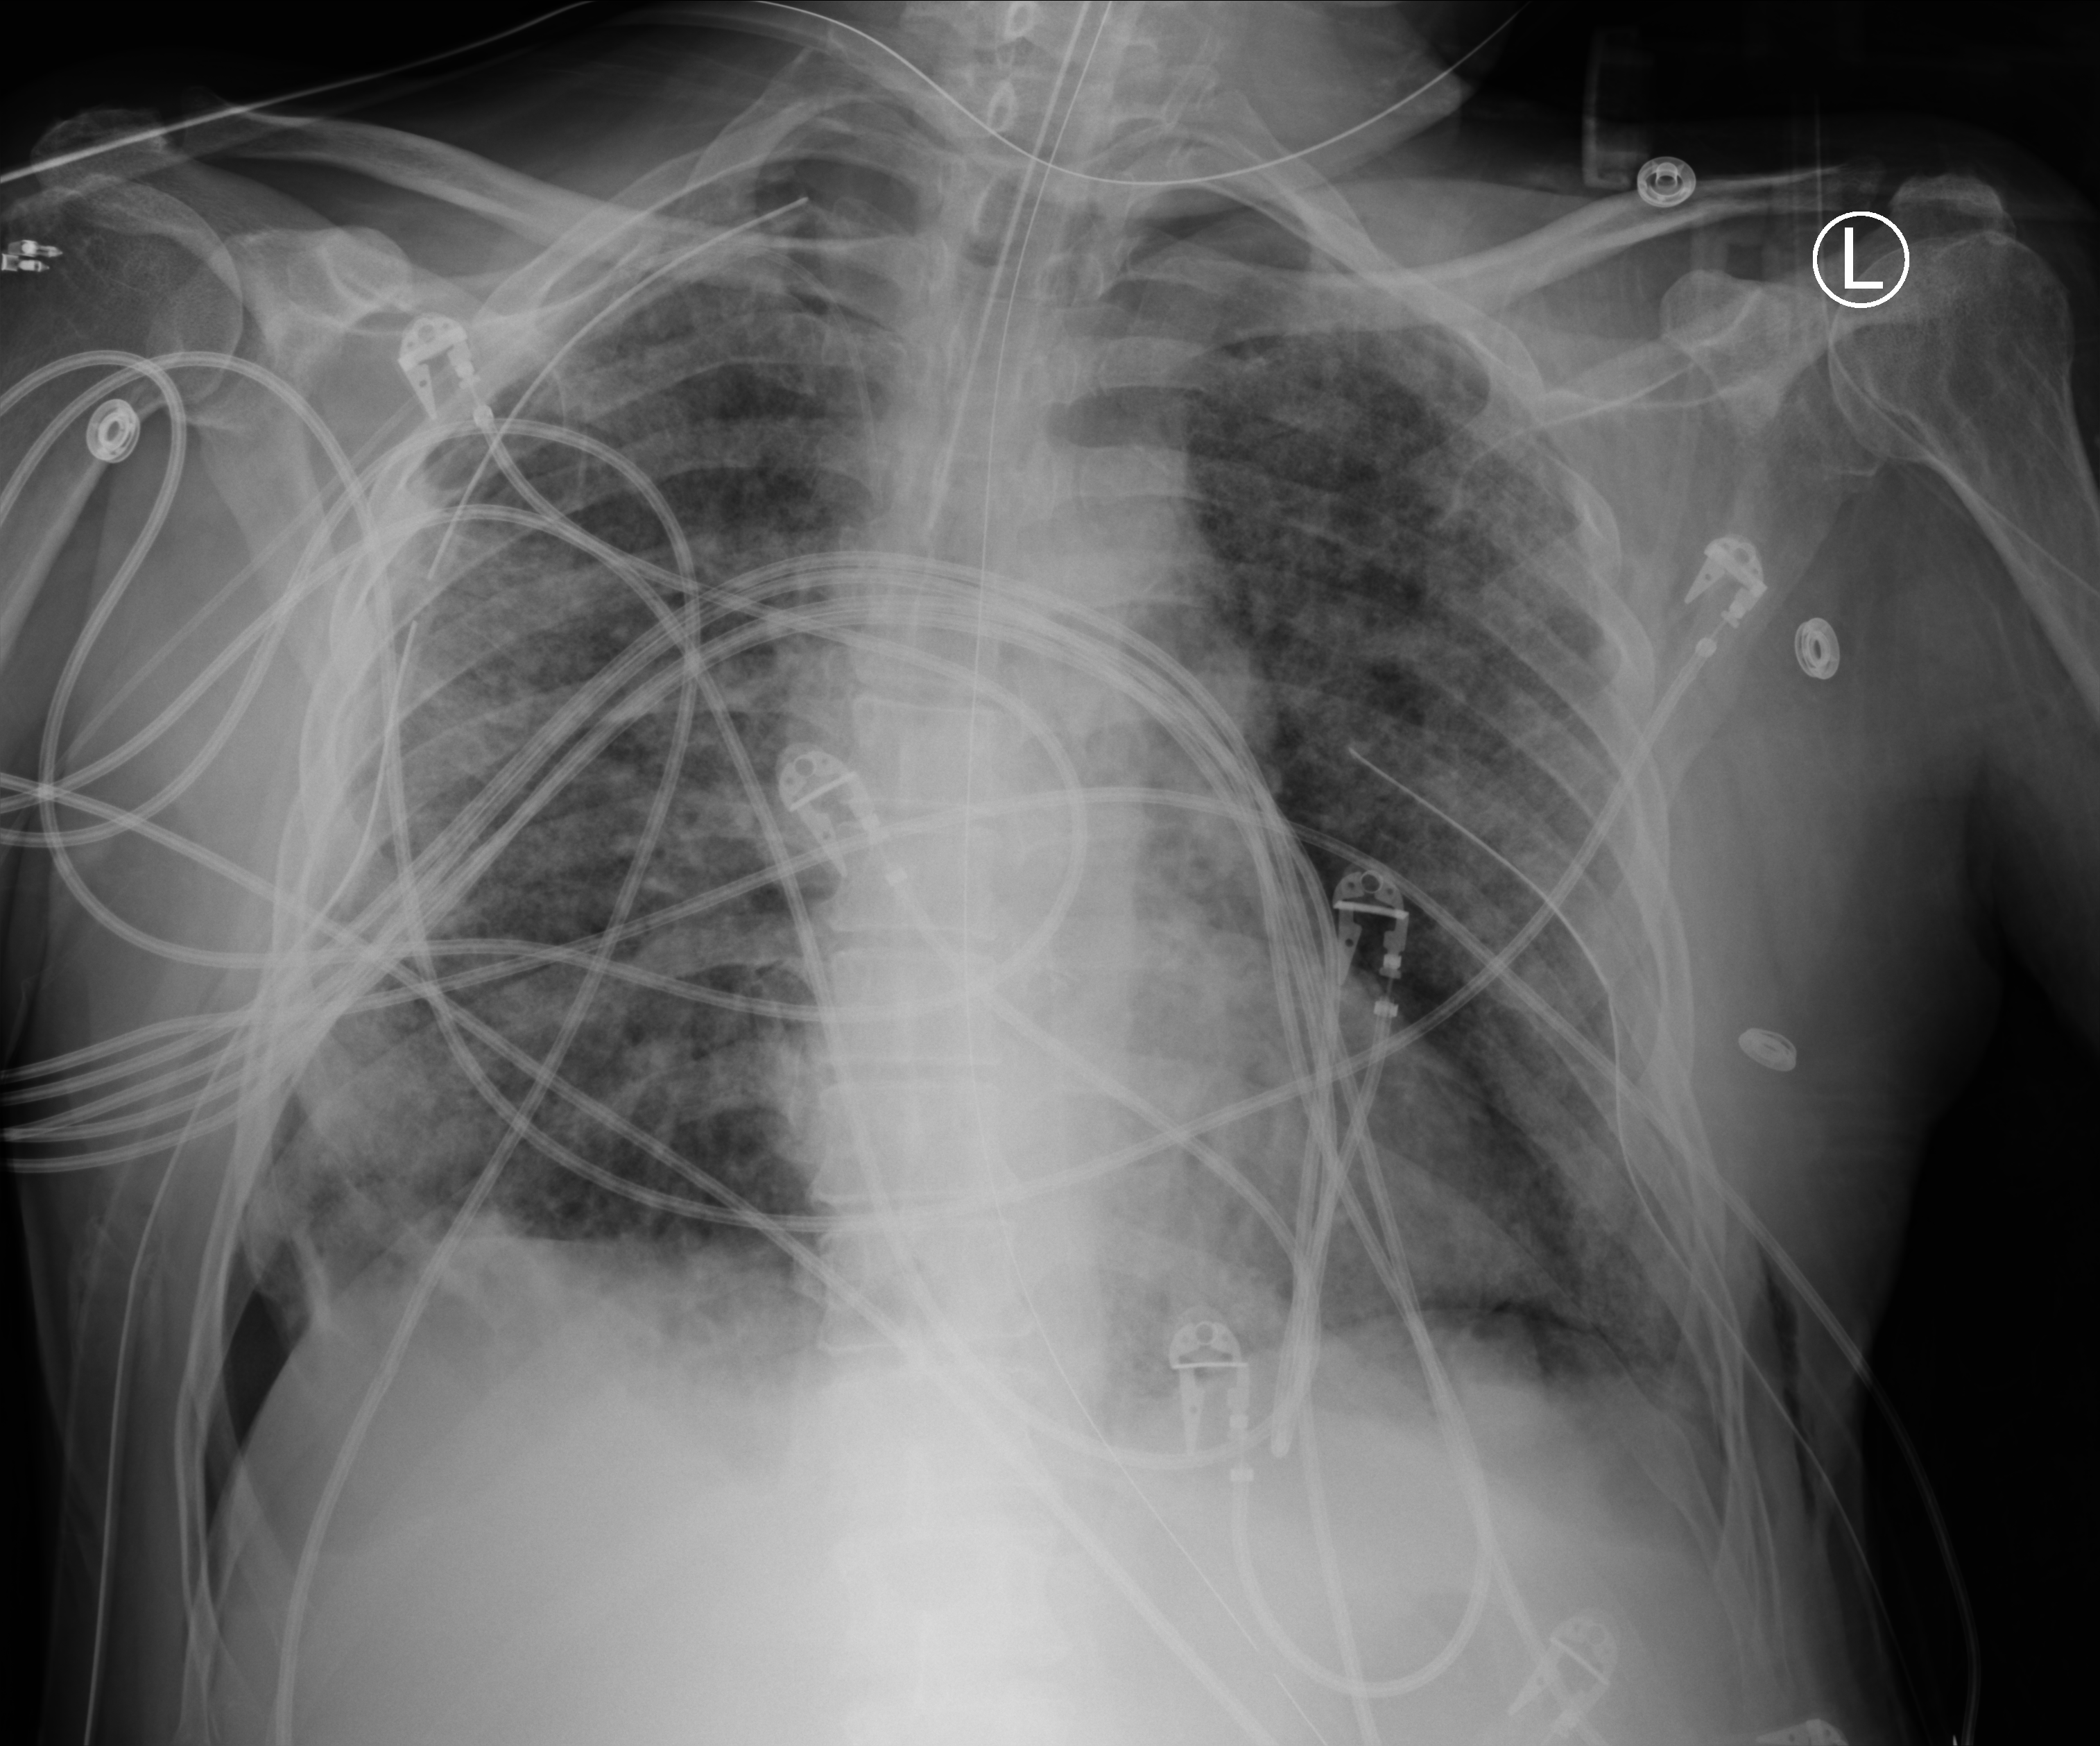
Portable chest radiograph, anteroposterior (AP) projection. Patient hospitalised with COVID-19; male, aged 60–74 years.
From the hospital-stay record, not from the radiograph (when in the stay this image was taken is not recorded): mechanically ventilated during this hospital stay: yes.